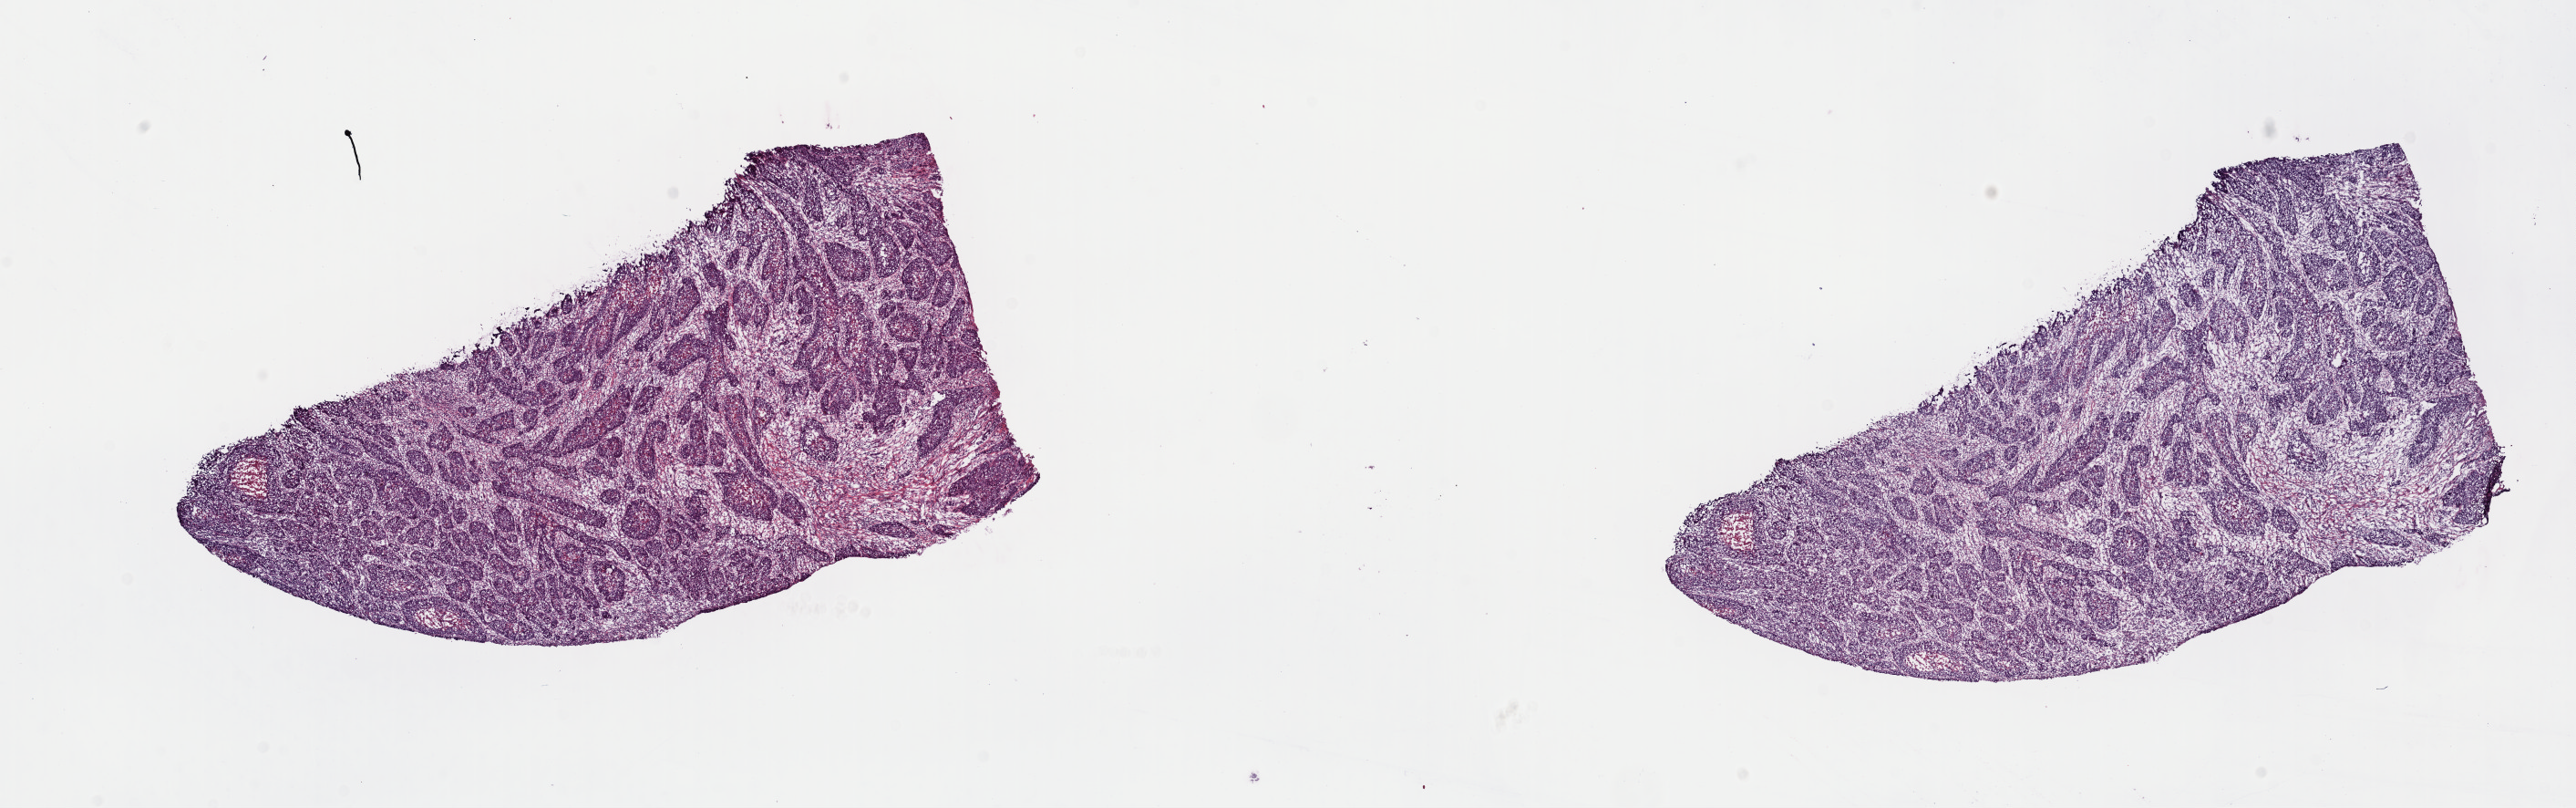
Digitized H&E tissue section (whole slide), a low-resolution overview of the entire scanned area, about 22.3 x 7.0 mm (slide scanned at 40x), frozen section from the top of the tissue portion, primary tumour sample from the head and neck. Male patient; age at initial diagnosis 69 years. Histologic grade: G3 (poorly differentiated). Slide review estimates, as recorded: tumour cells 33%, tumour nuclei 60%, normal cells 0%, stromal cells 50%, necrosis 17%. Inflammatory infiltration, as recorded: lymphocyte infiltration 8%, monocyte infiltration 2%, neutrophil infiltration 2%.
AJCC pathologic stage: IVA (7th edition). Diagnosis: Squamous cell carcinoma, NOS (mandible).